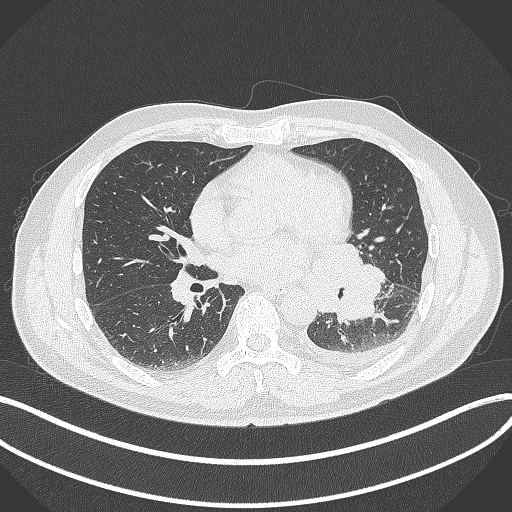
Chest CT, one axial slice. Position 169 of 342 along the scan axis. Reconstruction kernel B70f. Lung window (W 1500 / L -600 HU). 1 mm slice thickness. 512 × 512 image matrix, field of view 400 × 400 mm. Male patient, age 58 years. Case-level facts recorded for this patient, not image findings: clinical TNM (as recorded): T3 N1 M1b; histopathological grade: G3.
Structures marked on this image (bounding box drawn by a radiologist):
- lung tumour (recorded histology: small cell carcinoma): bounding box (x1, y1, x2, y2) in pixels: (315, 237, 383, 325)